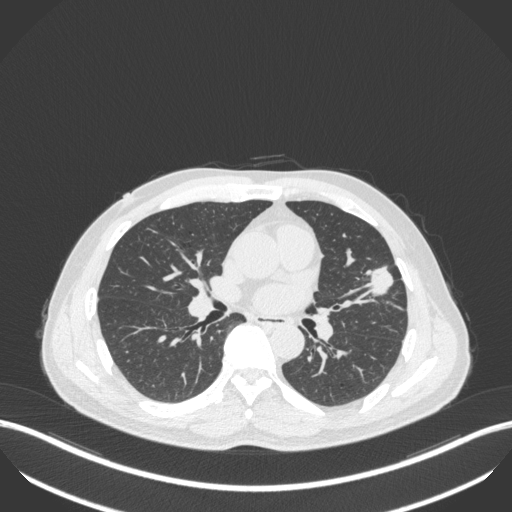
Chest CT, one axial slice; slice 211 of 418 in the series (ordered by position); reconstruction kernel B31f; lung window (W 1500 / L -600 HU); 512 × 512 image matrix, field of view 400 × 400 mm. Male patient, age 55 years. From the clinical record (not read from this slice): clinical TNM (as recorded): T1c N0 M0.
Outlined on this slice (bounding box drawn by a radiologist):
- lung tumour (recorded histology: adenocarcinoma): bounding box <362,264,397,299> (left, top, right, bottom; pixels)